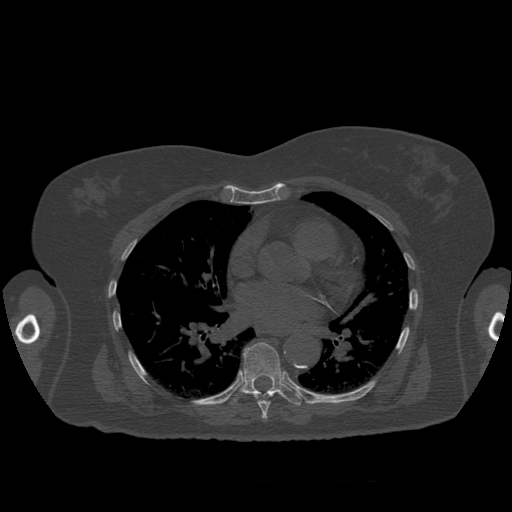
CT including the spine, one axial slice; slice 386 of 399 in the series (ordered by position); reconstruction kernel STANDARD; bone window (W 1800 / L 400 HU); 512 × 512 image matrix, field of view 404 × 404 mm. Patient age 81 years. From the clinical record (not read from this slice): primary cancer: renal; vertebrae with lytic lesions (as recorded): L1.
Annotated regions visible in this slice (semi-automatic segmentation, software-assisted and operator-edited):
- T7 vertebra: bounding box [x1, y1, x2, y2] px = [248, 393, 274, 420]
- T8 vertebra: [227, 343, 303, 406]